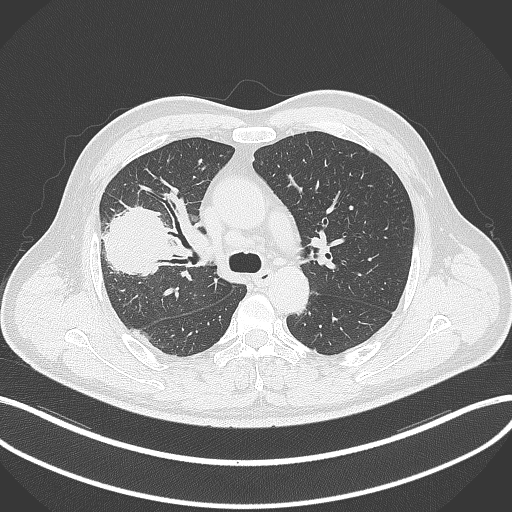
Chest CT, one axial slice; slice 220 of 348 in the series (ordered by position); lung window (W 1500 / L -600 HU); 1 mm slice thickness; 512 × 512 image matrix, field of view 400 × 400 mm. Patient: male, 55 years. From the clinical record (not read from this slice): clinical TNM (as recorded): T3 N2 M1.
Annotated regions visible in this slice (bounding box drawn by a radiologist):
- lung tumour (recorded histology: adenocarcinoma): bounding box [x1, y1, x2, y2] px = [96, 203, 173, 284]